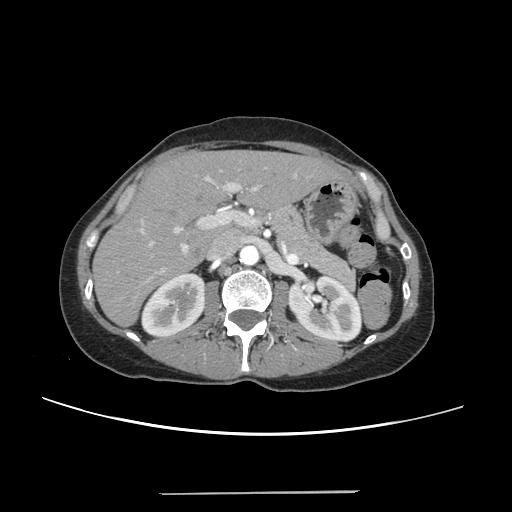
Contrast-enhanced abdominal CT, one axial slice. Position 139 of 240 along the scan axis. 120 kVp. Soft-tissue window (W 400 / L 40 HU). 1.25 mm slice thickness. 512 × 512 image matrix, field of view 371 × 371 mm. Female patient, age 60 years. From the clinical record (not read from this slice): diagnosis: colorectal cancer liver metastases, imaged before liver resection; multiple liver metastases: no; largest metastasis: 1.5 cm; disease in both lobes: no.
Annotated regions visible in this slice (outlined manually by an expert reader):
- liver: bounding box [x1, y1, x2, y2] px = [94, 152, 343, 325]
- planned liver remnant (the part of the liver to remain after resection): [94, 152, 342, 324]
- portal vein (with intrahepatic branches): [139, 171, 297, 281]